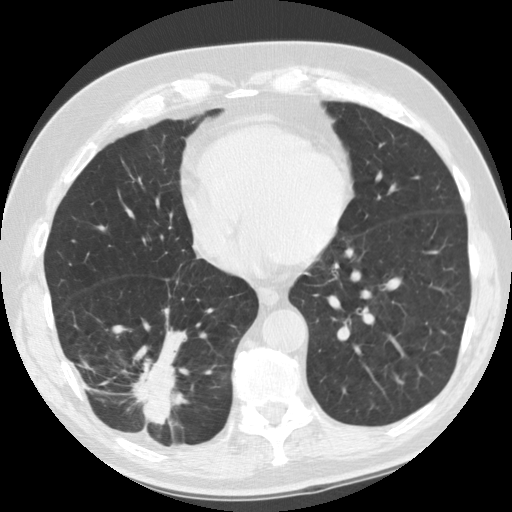
Low-dose screening chest CT, axial slice; baseline annual screen; lung window (W 1500 / L -600 HU); 2.5 mm slice thickness; slice 93 of 135 in the series. Male participant, aged 69 years at enrolment.
Lesion marked by an expert reader, bounding box [x1, y1, x2, y2] px = [104, 331, 190, 440]. The screening reader recorded 2 non-calcified nodules or masses ≥4 mm on this exam (right lower lobe, right lower lobe); which of them this box marks is not recorded. Official screen result: positive, change unspecified: nodule(s) >= 4 mm or enlarging nodule(s), mass(es), or other non-specific abnormalities suspicious for lung cancer.